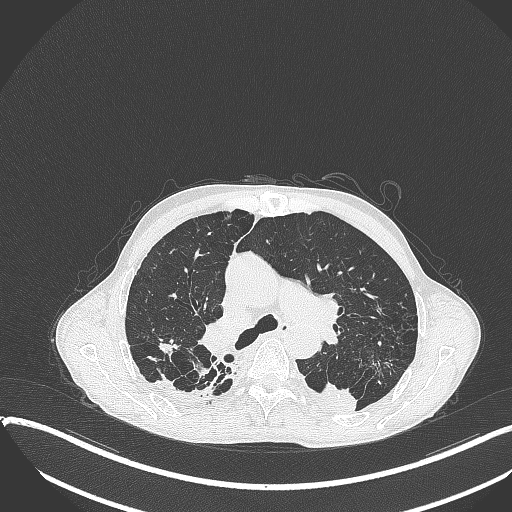
Chest CT, one axial slice. Slice 255 of 401 in the series (ordered by position). Reconstruction kernel B70f. Lung window (W 1500 / L -600 HU). 1 mm slice thickness. 512 × 512 image matrix, field of view 400 × 400 mm. Patient: male, 57 years. From the clinical record (not read from this slice): clinical TNM (as recorded): T4 N0 M0.
Annotated regions visible in this slice (bounding box drawn by a radiologist):
- lung tumour (recorded histology: squamous cell carcinoma): bounding box <307,375,359,418> (left, top, right, bottom; pixels)